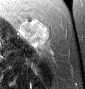
MRI of an extremity soft-tissue mass, one axial slice; slice 27 of 46 in the series (ordered by position); T2-weighted fat-saturated; MR volume resampled by the dataset authors to the PET/CT grid (not the native acquisition matrix); 3.27 mm slice thickness; 85 × 89 image matrix. Female patient. From the clinical record (not read from this slice): histological type: leiomyosarcoma; grade: intermediate; site of the primary tumour: parascapusular.
Outlined on this slice (expert contour drawn on MRI and transferred to this co-registered scan by the dataset authors):
- gross tumour volume including surrounding oedema: box from (x=20, y=18) to (x=51, y=49) px
- gross tumour volume (mass): (x=22, y=18)–(x=49, y=43)